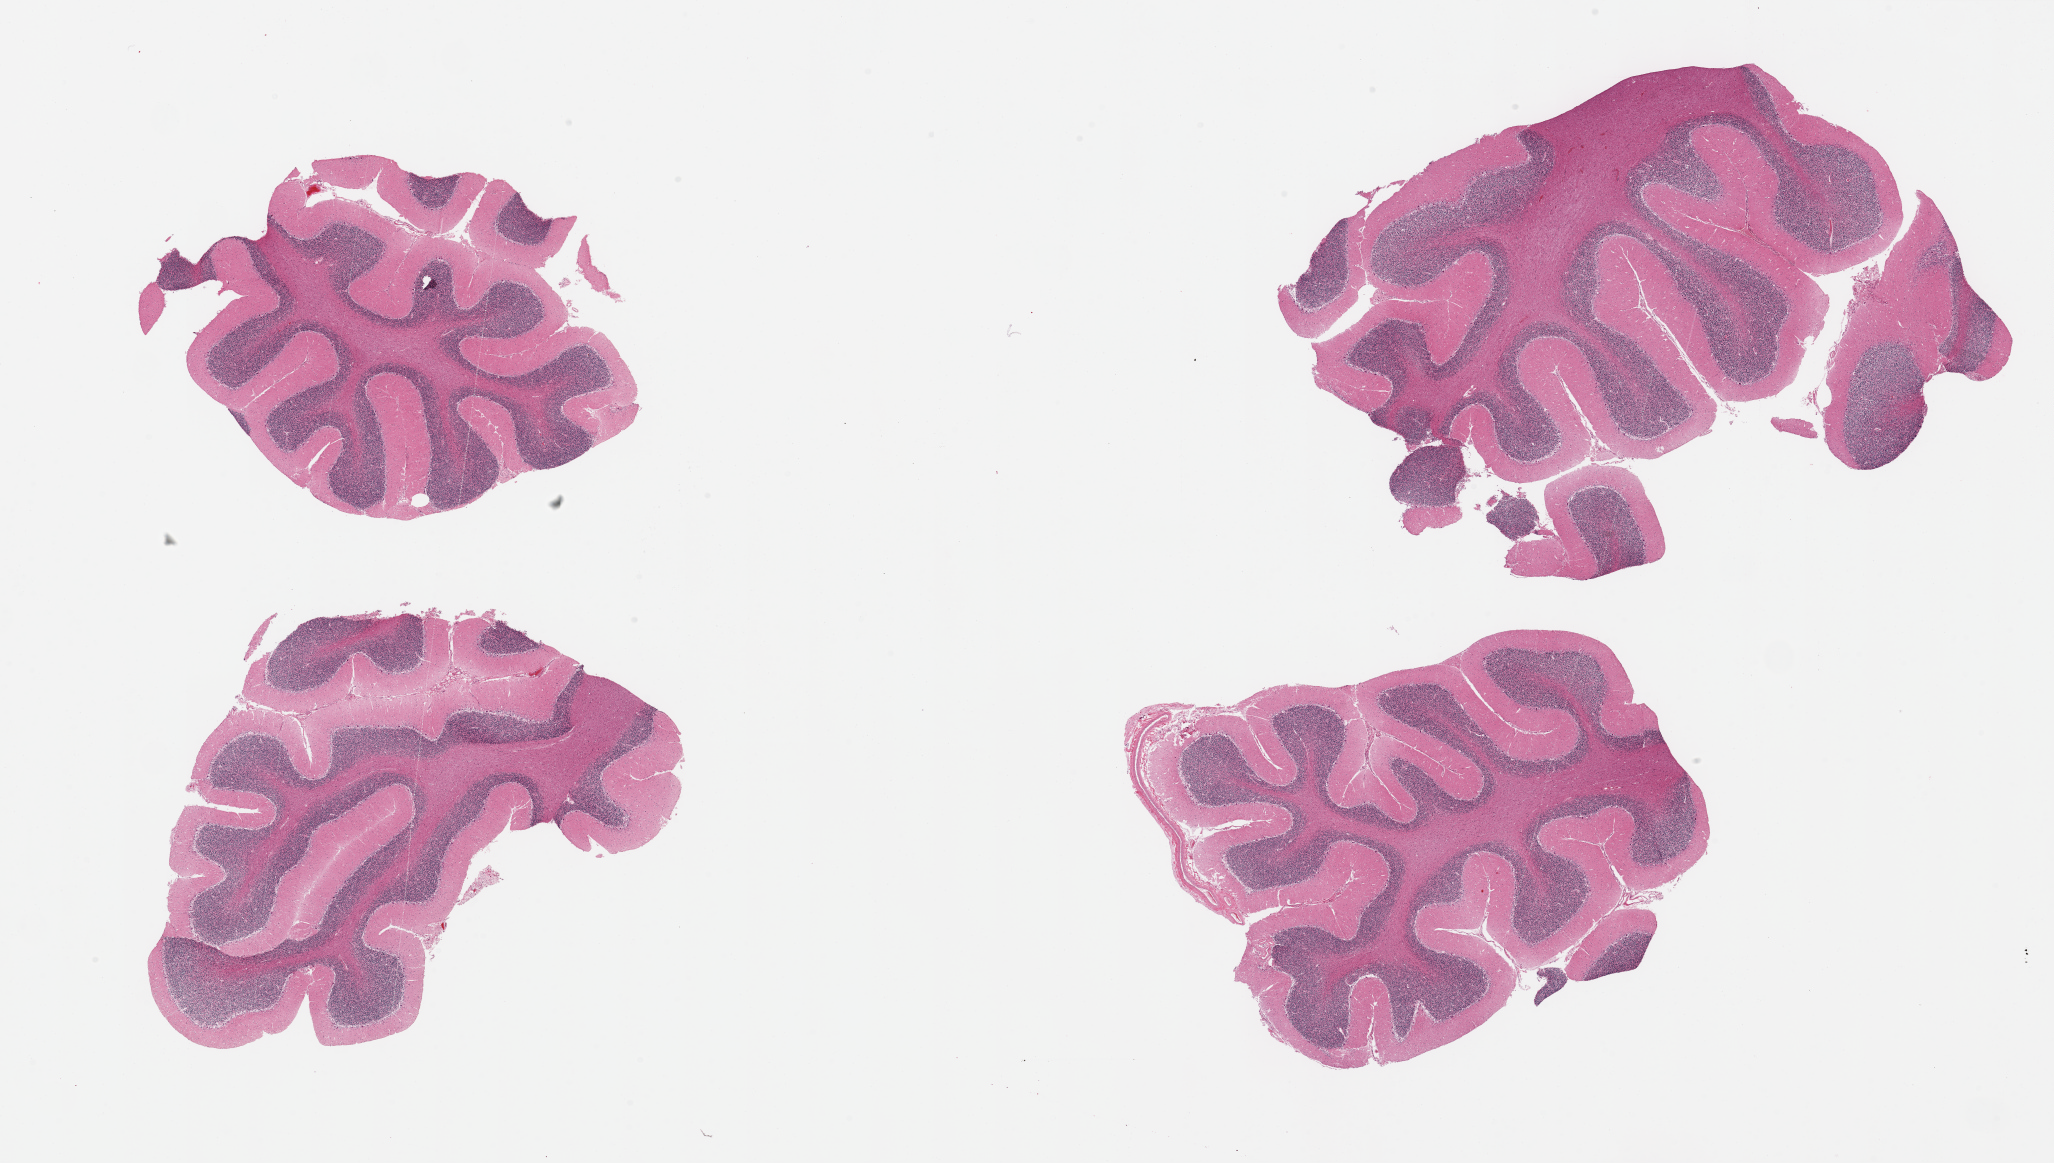
Whole-slide image, haematoxylin and eosin stain, a low-resolution overview of the entire scanned area, about 32.5 x 18.4 mm (acquisition: 20x scan). PAXgene-fixed paraffin-embedded (PFPE) section. Section of cerebellum (target tissue). Donor tissue sample. Donor sex: male.
Reviewer comment on this tissue sample: 4 pieces; Purkinje cells present.